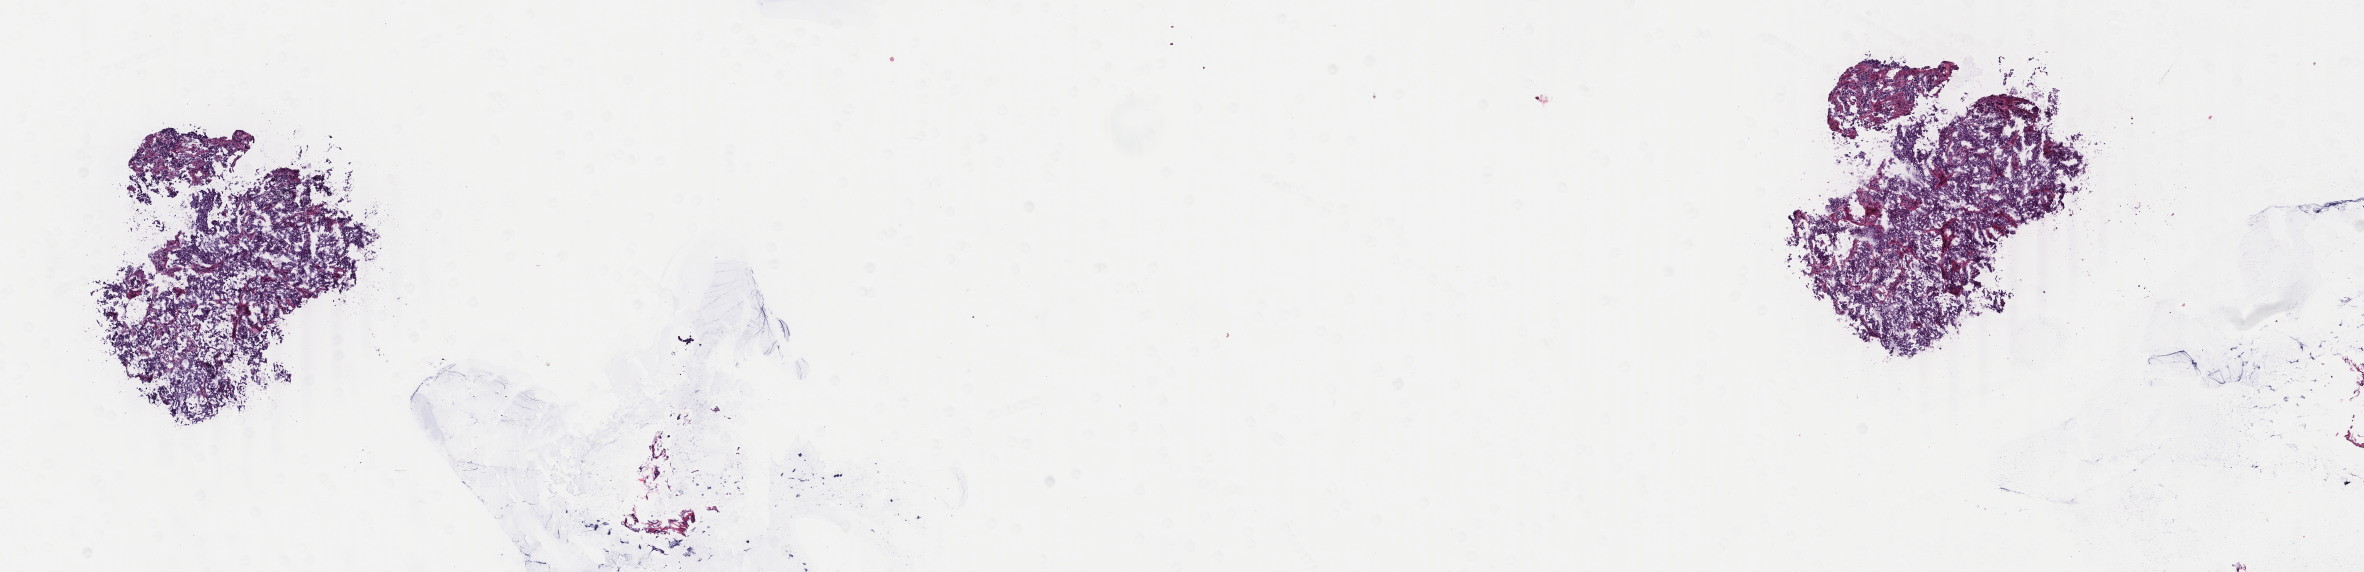
Digitized H&E tissue section (whole slide) — a low-resolution overview of the entire scanned area, about 18.8 x 4.5 mm (slide scanned at 40x); frozen section from the bottom of the tissue portion; sample: primary tumour, breast. Patient: female, age at initial diagnosis 36 years. Composition of this section per pathologist review: tumour cells 90%, tumour nuclei 75%, normal cells 0%, stromal cells 9%, necrosis 1%. Inflammatory infiltration, as recorded: lymphocyte infiltration 12%, monocyte infiltration 0%, neutrophil infiltration 0%.
* AJCC pathologic stage: IIIC (6th edition)
* laterality: left
* histologic diagnosis: Infiltrating duct carcinoma, NOS
* lymph nodes positive (case pathology): 18 of 20 examined